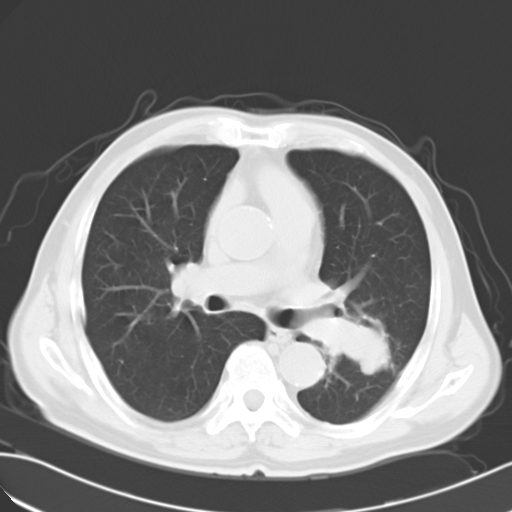
Chest CT, one axial slice. Slice 16 of 28 in the series (ordered by position). Reconstruction kernel B40f. Lung window (W 1500 / L -600 HU). 10 mm slice thickness. 512 × 512 image matrix, field of view 353 × 353 mm. Male patient, age 63 years. From the clinical record (not read from this slice): clinical TNM (as recorded): T3 N3 M1a; histopathological grade: G3.
Outlined on this slice (bounding box drawn by a radiologist):
- lung tumour (recorded histology: large cell carcinoma): bounding box (x1, y1, x2, y2) in pixels: (294, 301, 401, 388)